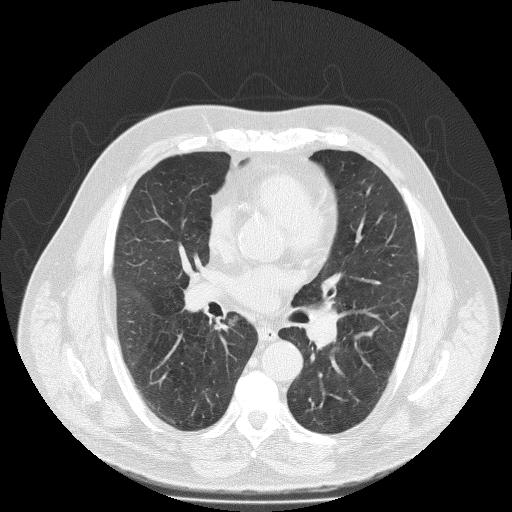
Chest CT (low-dose screening protocol), one axial image, first (baseline) screen, lung window (W 1500 / L -600 HU), 2 mm slice thickness, 512 × 512 image matrix, field of view 430 × 430 mm. Male, age 65 years at enrolment. Former smoker at enrolment.
- Expert reader's lesion annotation, box from (x=210, y=307) to (x=248, y=334) px.
- The screening reader recorded 2 non-calcified nodules or masses ≥4 mm on this exam; which of them this box marks is not recorded.
- Lung cancer was diagnosed 651 days after this screen (after the second annual screen): large cell neuroendocrine carcinoma, right lower lobe, undifferentiated (G4), stage IIIA (AJCC 6th edition).